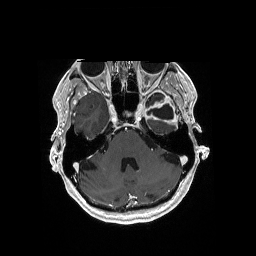
Brain MRI from a brain-tumour surgery series, one axial slice. Slice 130 of 176 in the series (ordered by position). T1-weighted post-contrast. 256 × 256 image matrix, field of view 256 × 256 mm. Case-level facts recorded for this patient, not image findings: histopathology: Glioblastoma; WHO grade: 4; IDH mutation: no; tumour location: Left Medial Temporal.
Outlined on this slice (outlined manually by an expert reader):
- previous resection cavity: bounding box (x1, y1, x2, y2) in pixels: (148, 104, 174, 119)
- tumour: (151, 116, 177, 126)